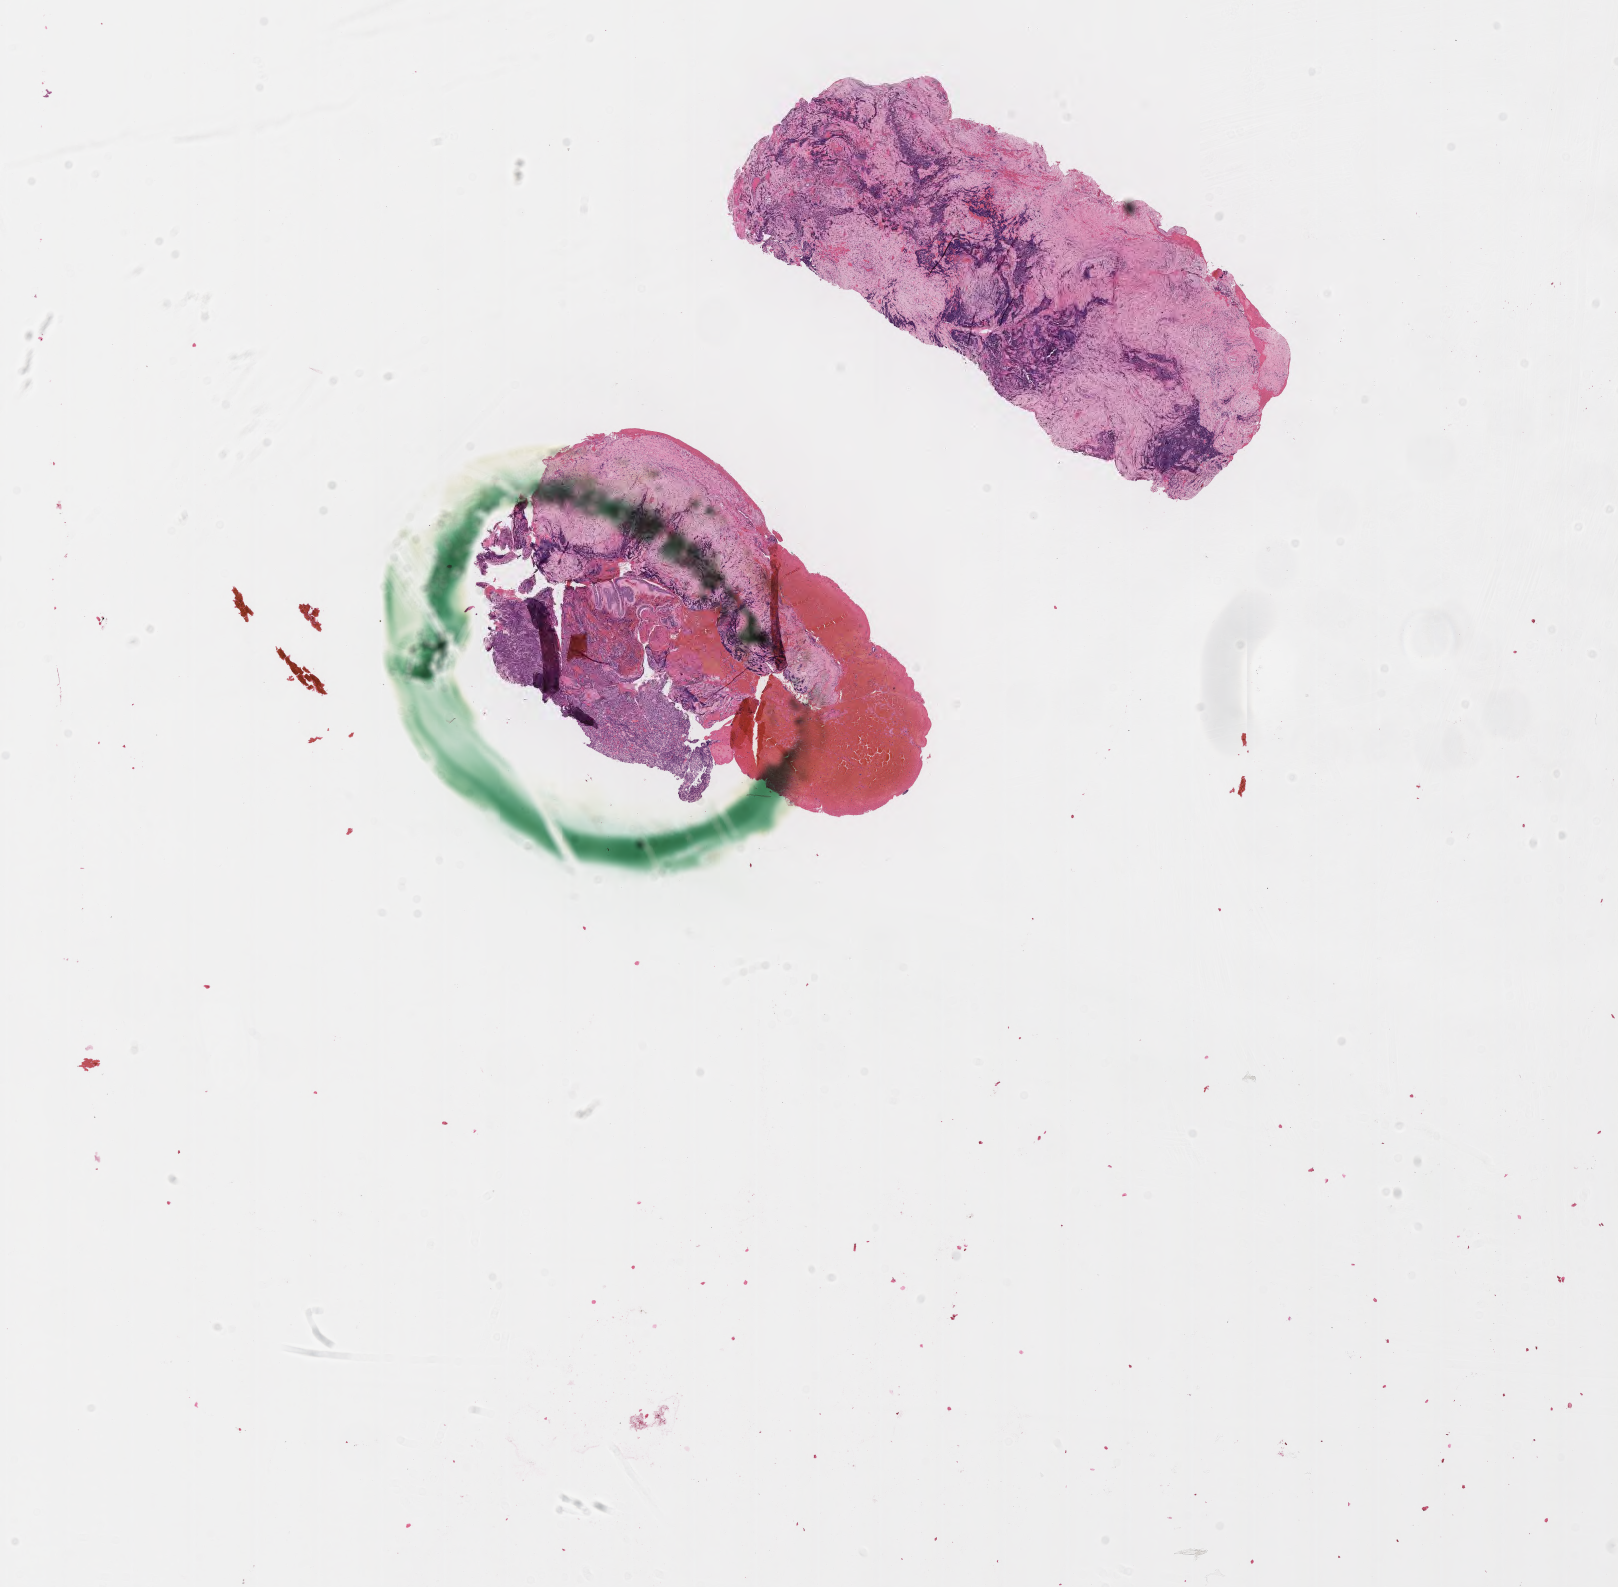
H&E whole-slide image of tumor tissue from the nasal cavity, low-resolution overview of the scanned area, about 13.1 x 12.8 mm, formalin-fixed paraffin-embedded section. Patient male; age 171 months.
• recorded diagnosis: Alveolar rhabdomyosarcoma